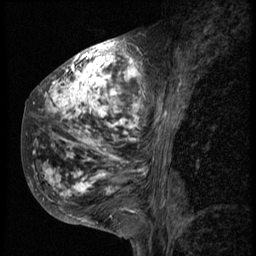
Breast MRI (dynamic contrast-enhanced), one sagittal slice; position 23 of 58 along the scan axis; 3 images stored at this slice position (order not interpretable as contrast timing); 1.5 T; TE 4.2 ms, TR 9 ms; 2.5 mm slice thickness; 256 × 256 image matrix, field of view 180 × 180 mm. Female patient, age 50 years. Case-level facts recorded for this patient, not image findings: setting: breast cancer imaged before/during neoadjuvant chemotherapy; receptor status: triple-negative.
Outlined on this slice (semi-automatically segmented with operator editing):
- analysis volume of interest (the breast-tissue region the enhancement analysis was run in; not a lesion): bounding box <23,48,172,214> (left, top, right, bottom; pixels)
- tumour enhancement mask (voxels above the 140 % enhancement threshold inside the analysis volume of interest): <31,52,171,213>